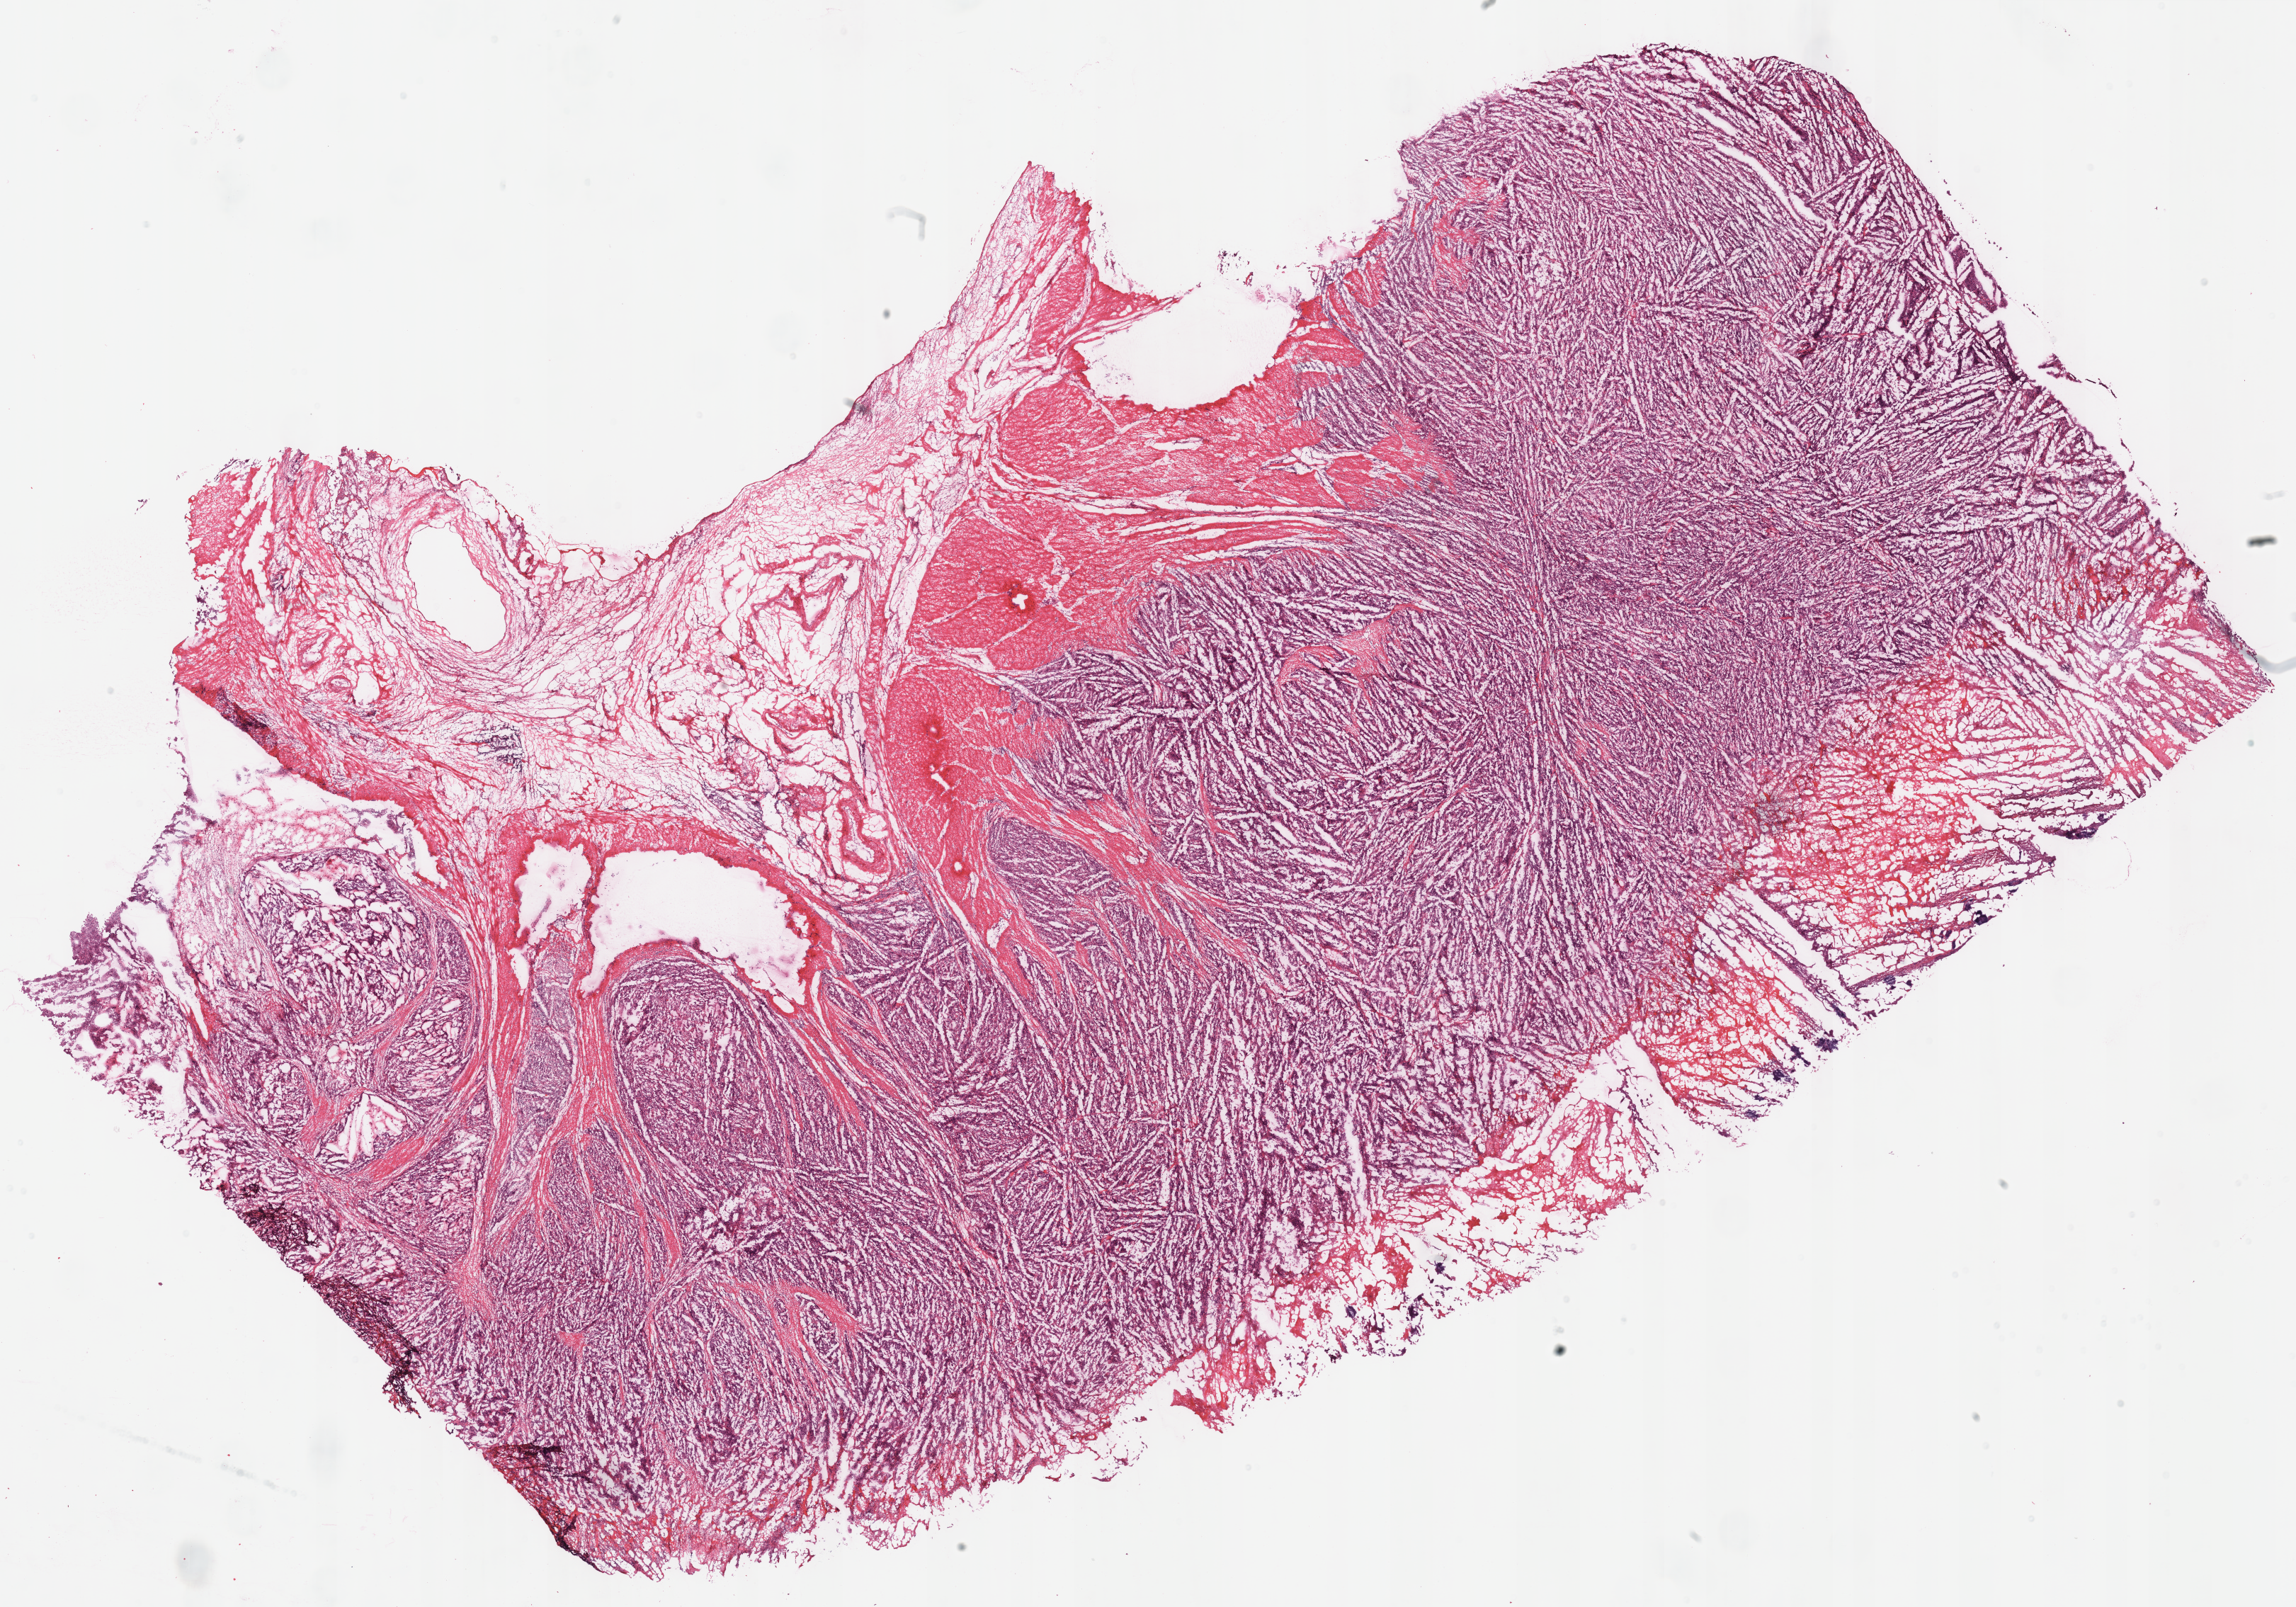
H&E-stained whole-slide image — whole scanned area (about 25.5 x 17.9 mm, slide scanned at 40x) shown as a low-resolution overview, frozen section from the top of the tissue portion, sample: primary tumour, stomach. Patient: male, age at initial diagnosis 59 years. Histologic grade: G3 (poorly differentiated). Slide review estimates, as recorded: tumour cells 73%, tumour nuclei 75%, normal cells 9%, stromal cells 11%, necrosis 7%. Infiltration values recorded for this section: lymphocyte infiltration 10%, monocyte infiltration 0%, neutrophil infiltration 5%.
Histologic diagnosis: Adenocarcinoma, intestinal type (gastric antrum). AJCC pathologic stage: IIIB (7th edition). Lymph nodes positive (case pathology): 10 of 10 examined.